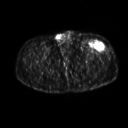
FDG PET of an extremity soft-tissue mass (from a PET/CT study), one axial slice. Slice 255 of 267 in the series (ordered by position). 3.27 mm slice thickness. 128 × 128 image matrix, field of view 500 × 500 mm. Patient: male, 64 years. Case-level facts recorded for this patient, not image findings: histological type: extraskeletal osteosarcoma; grade: high; site of the primary tumour: thigh.
Outlined on this slice (expert contour drawn on MRI and transferred to this co-registered scan by the dataset authors):
- gross tumour volume (mass): bounding box <91,42,105,49> (left, top, right, bottom; pixels)